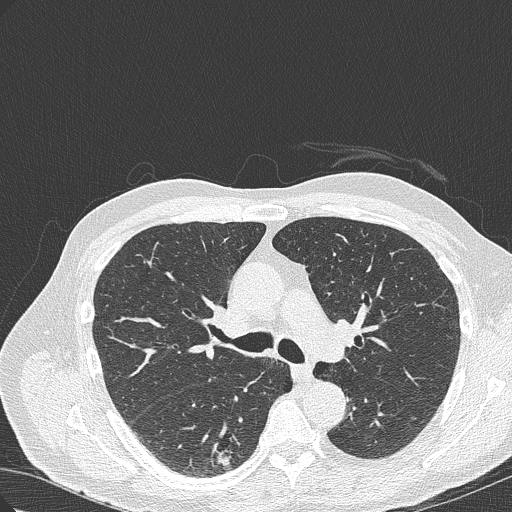
Chest CT (low-dose screening protocol), one axial image, first (baseline) screen, lung window (W 1500 / L -600 HU), 1 mm slice thickness. Male participant, aged 70 years at enrolment. Current smoker at enrolment.
Lesion marked by an expert reader, bounding box (x1, y1, x2, y2) in pixels: (200, 419, 264, 468). The screening reader recorded 4 non-calcified nodules or masses ≥4 mm on this exam (right lower lobe, right lower lobe, right upper lobe, right lower lobe); which of them this box marks is not recorded. Official screen result: positive, change unspecified: nodule(s) >= 4 mm or enlarging nodule(s), mass(es), or other non-specific abnormalities suspicious for lung cancer. Participant outcome: lung cancer diagnosed 978 days after this screen (after the third annual screen) — bronchiolo-alveolar adenocarcinoma, NOS, right lower lobe, poorly differentiated (G3), stage IB (AJCC 6th edition), 30 mm at pathology.